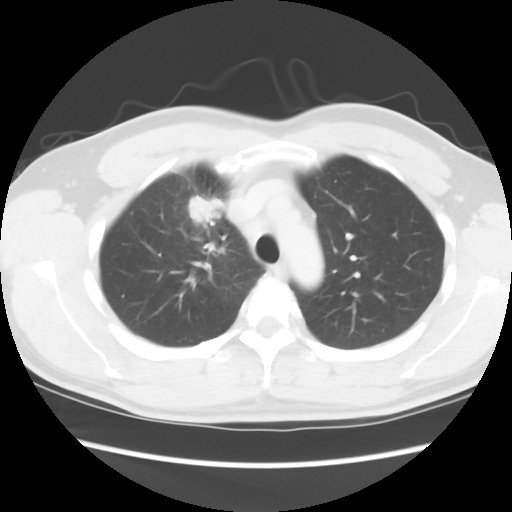
Chest CT, one axial slice; slice 66 of 80 in the series (ordered by position); reconstruction kernel STANDARD; 120 kVp; lung window (W 1500 / L -600 HU); 5 mm slice thickness; 512 × 512 image matrix, field of view 360 × 360 mm. Male patient, age 35 years. From the clinical record (not read from this slice): clinical TNM (as recorded): T1c N1 M1b.
Structures marked on this image (bounding box drawn by a radiologist):
- lung tumour (recorded histology: adenocarcinoma): bounding box (x1, y1, x2, y2) in pixels: (187, 191, 228, 231)